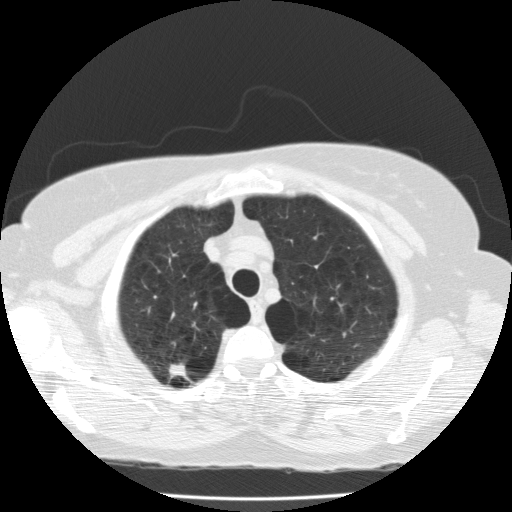
Chest CT (low-dose screening protocol), one axial image. Second screening round (one year after baseline). Lung window (W 1500 / L -600 HU). Standard (soft-tissue) reconstruction kernel (FC10). Slice 27 of 174 in the series. 512 × 512 image matrix, field of view 337 × 337 mm. Female participant, aged 59 years at enrolment. Current smoker at enrolment.
Lesion marked by an expert reader, bounding box <143,350,200,394> (left, top, right, bottom; pixels). The exam's reader record, not a measurement of the box and not confirmed to be the same lesion: non-calcified nodule or mass ≥4 mm, right upper lobe, 11 × 6 mm, spiculated (stellate) margins, soft tissue attenuation, pre-existing on the prior screen: yes; interval growth: no. Official screen result: positive, no significant change: stable abnormalities potentially related to lung cancer, unchanged since the prior screening exam. Lung cancer was diagnosed 490 days after this screen: adenocarcinoma, NOS, right upper lobe, poorly differentiated (G3), stage IA (AJCC 6th edition), 20 mm at pathology.